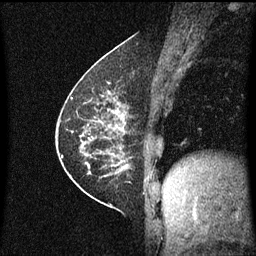
Breast MRI (dynamic contrast-enhanced), one sagittal slice. Slice 27 of 60 in the series (ordered by position). Dynamic contrast-enhanced series, image 2 of 3 at this slice position (ordered by acquisition). 1.5 T. TE 4.2 ms, TR 8.4 ms. 2 mm slice thickness. 256 × 256 image matrix, field of view 200 × 200 mm. Female patient, age 60 years.
Structures marked on this image (semi-automatic segmentation, software-assisted and operator-edited):
- analysis volume of interest (the breast-tissue region the enhancement analysis was run in; not a lesion): bounding box [x1, y1, x2, y2] px = [69, 66, 140, 193]
- tumour enhancement mask (voxels above the 70 % enhancement threshold inside the analysis volume of interest): [70, 70, 129, 175]